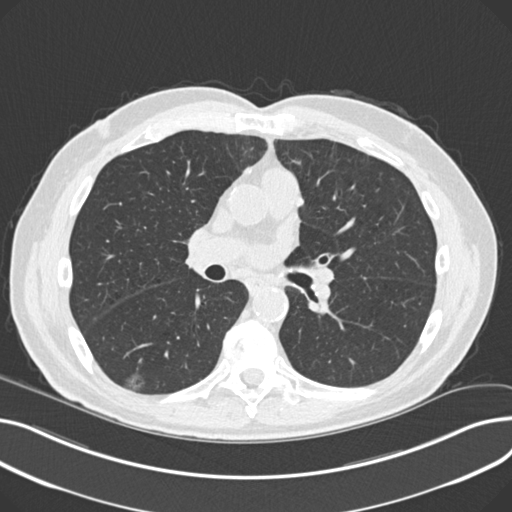
Low-dose screening chest CT, axial slice. Third screening round (two years after baseline). Lung window (W 1500 / L -600 HU). 2 mm slice thickness. Standard (soft-tissue) reconstruction kernel (B30f). Male, age 68 years at enrolment. Current smoker at enrolment.
- Lesion marked by an expert reader, box from (x=123, y=365) to (x=157, y=397) px.
- The screening reader recorded 5 non-calcified nodules or masses ≥4 mm on this exam; which of them this box marks is not recorded.
- Participant outcome: lung cancer diagnosed 247 days after this screen — non-small cell carcinoma, right lower lobe, poorly differentiated (G3), stage IA (AJCC 6th edition), 23 mm at pathology.